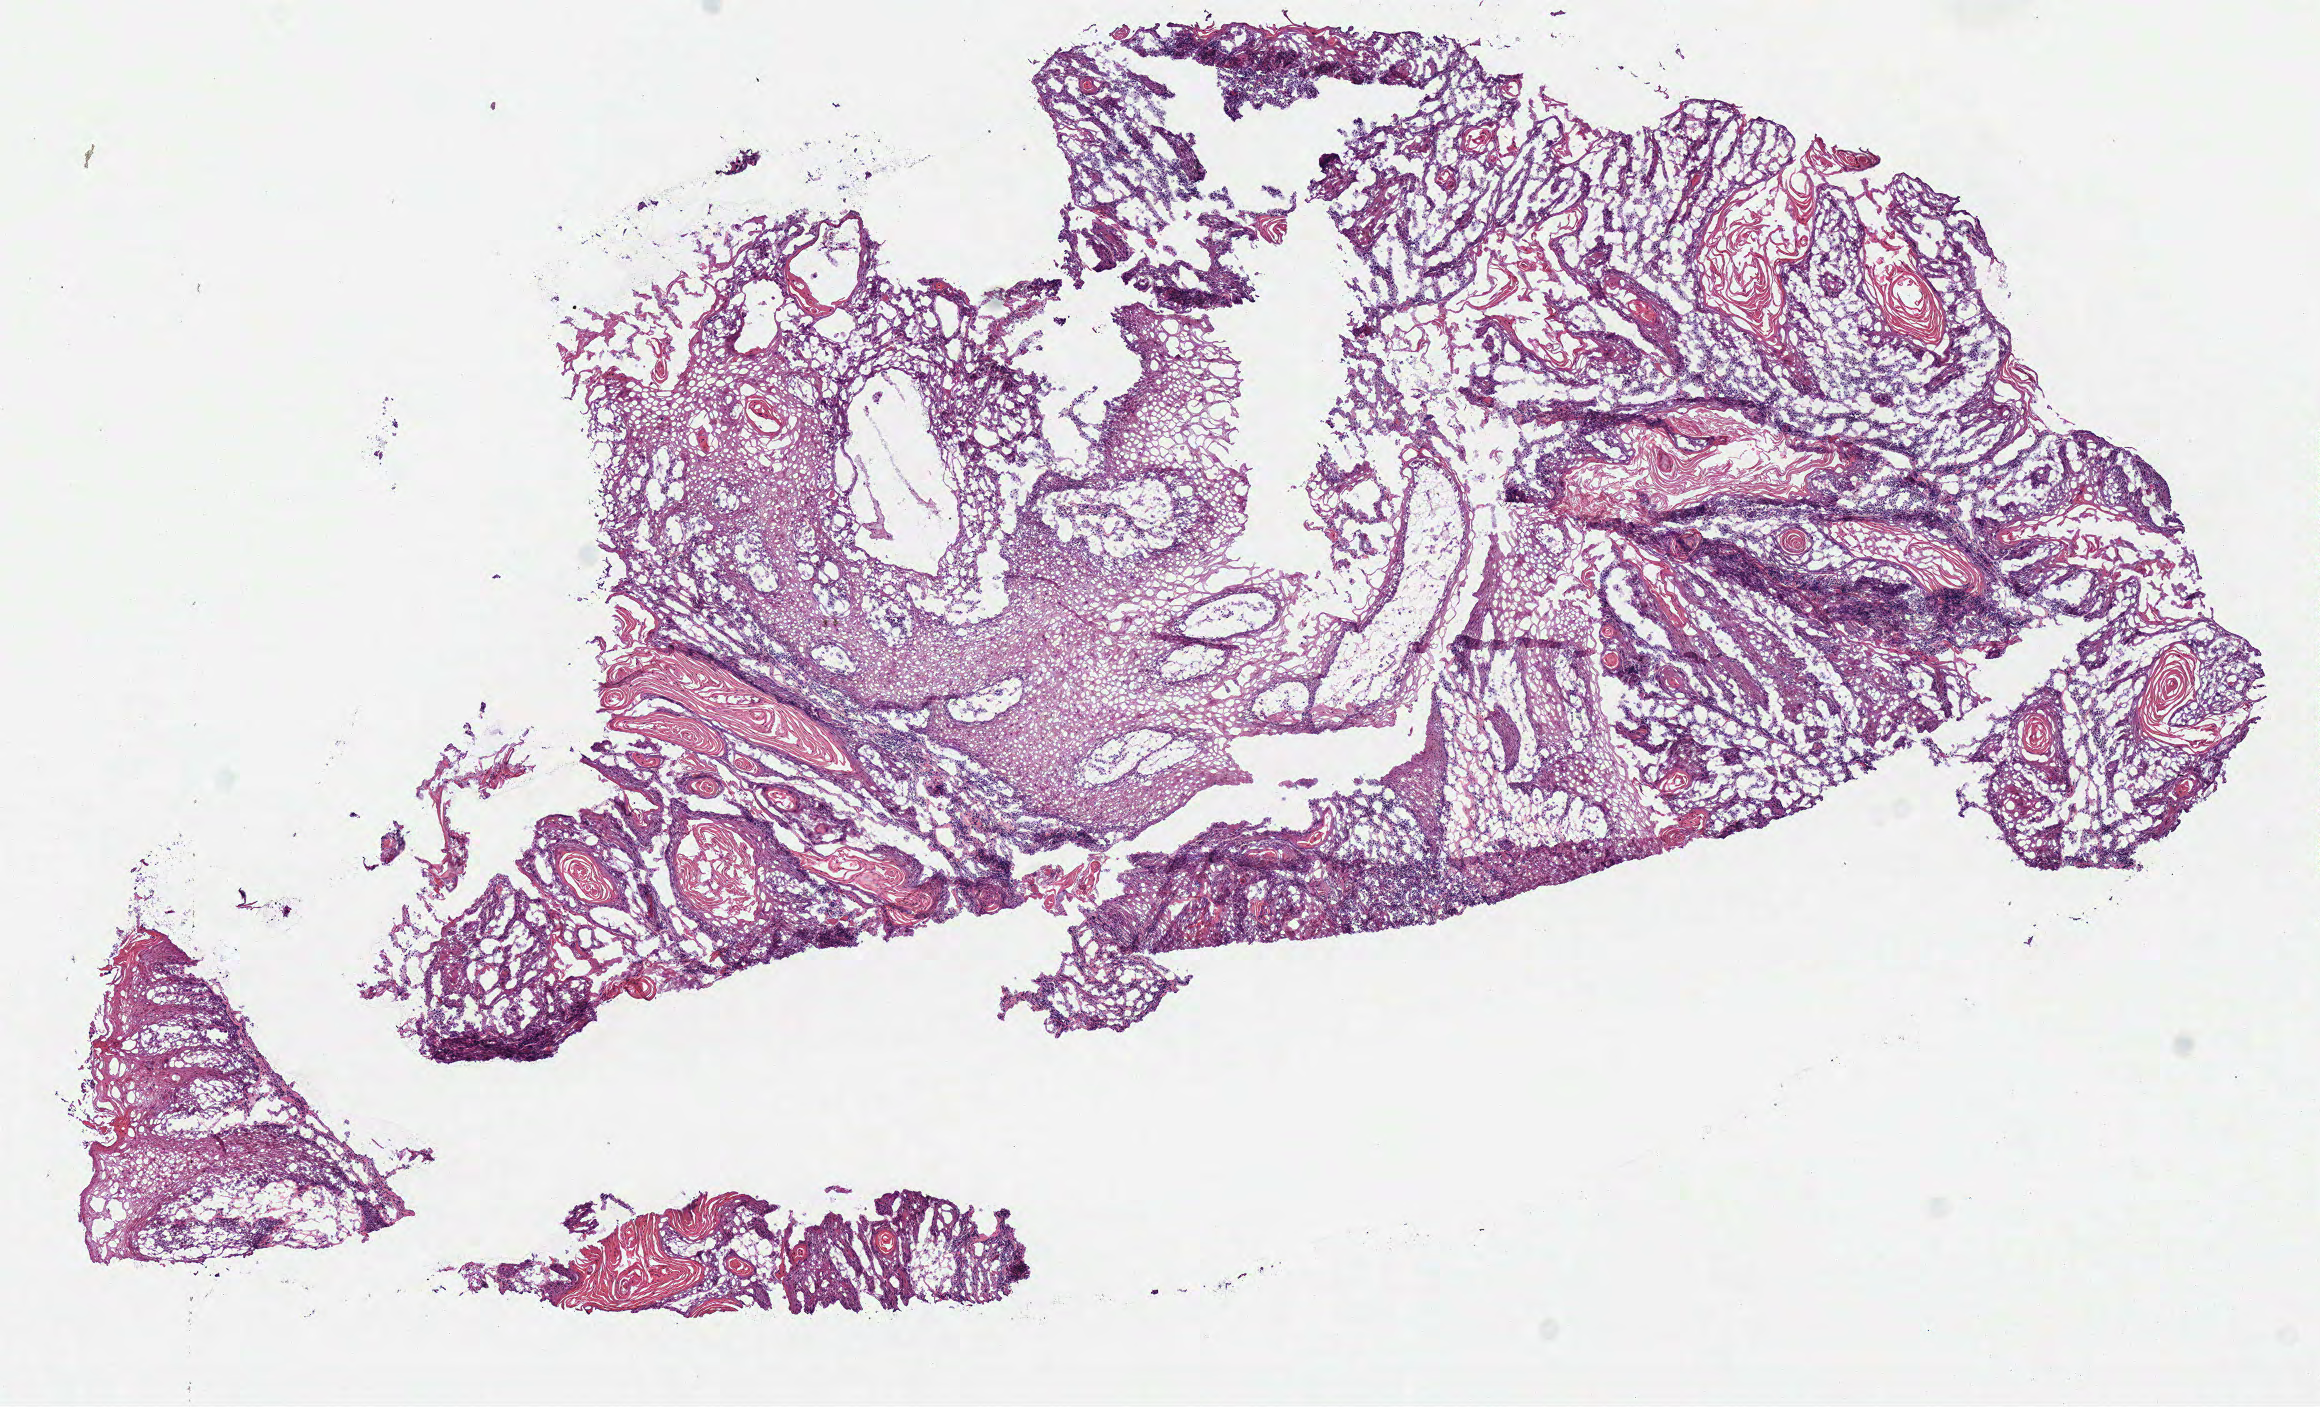
Digitized H&E-stained tissue section (whole slide) — whole scanned area (about 9.1 x 5.5 mm, from a 40x scan) shown as a low-resolution overview. Frozen section from the bottom of the tissue portion. Primary tumour sample from the head and neck. Male patient; age at initial diagnosis 34 years. Histologic grade: G2 (moderately differentiated). Pathologist review of this section (percent, as recorded): tumour cells 90%, tumour nuclei 85%, normal cells 0%, stromal cells 10%, necrosis 0%. Infiltration values recorded for this section: lymphocyte infiltration 8%, monocyte infiltration 1%, neutrophil infiltration 0%.
Histologic diagnosis: Squamous cell carcinoma, NOS. AJCC pathologic stage: II (7th edition).